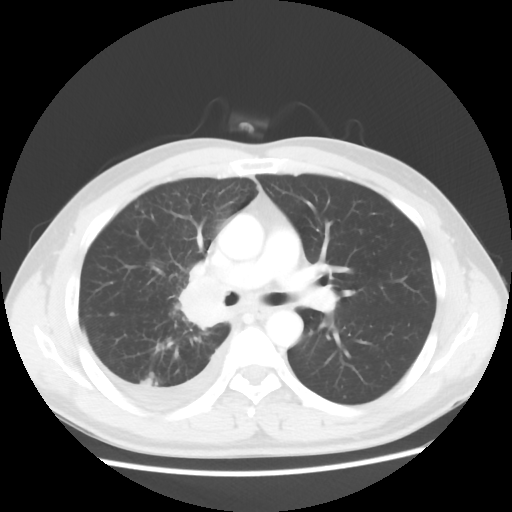
Chest CT, one axial slice; slice 33 of 56 in the series (ordered by position); reconstruction kernel STANDARD; lung window (W 1500 / L -600 HU); 5 mm slice thickness; 512 × 512 image matrix, field of view 360 × 360 mm. Patient: male, 46 years. From the clinical record (not read from this slice): clinical TNM (as recorded): T2 N3 M1.
Structures marked on this image (bounding box drawn by a radiologist):
- lung tumour (recorded histology: adenocarcinoma): bounding box (x1, y1, x2, y2) in pixels: (175, 272, 228, 335)